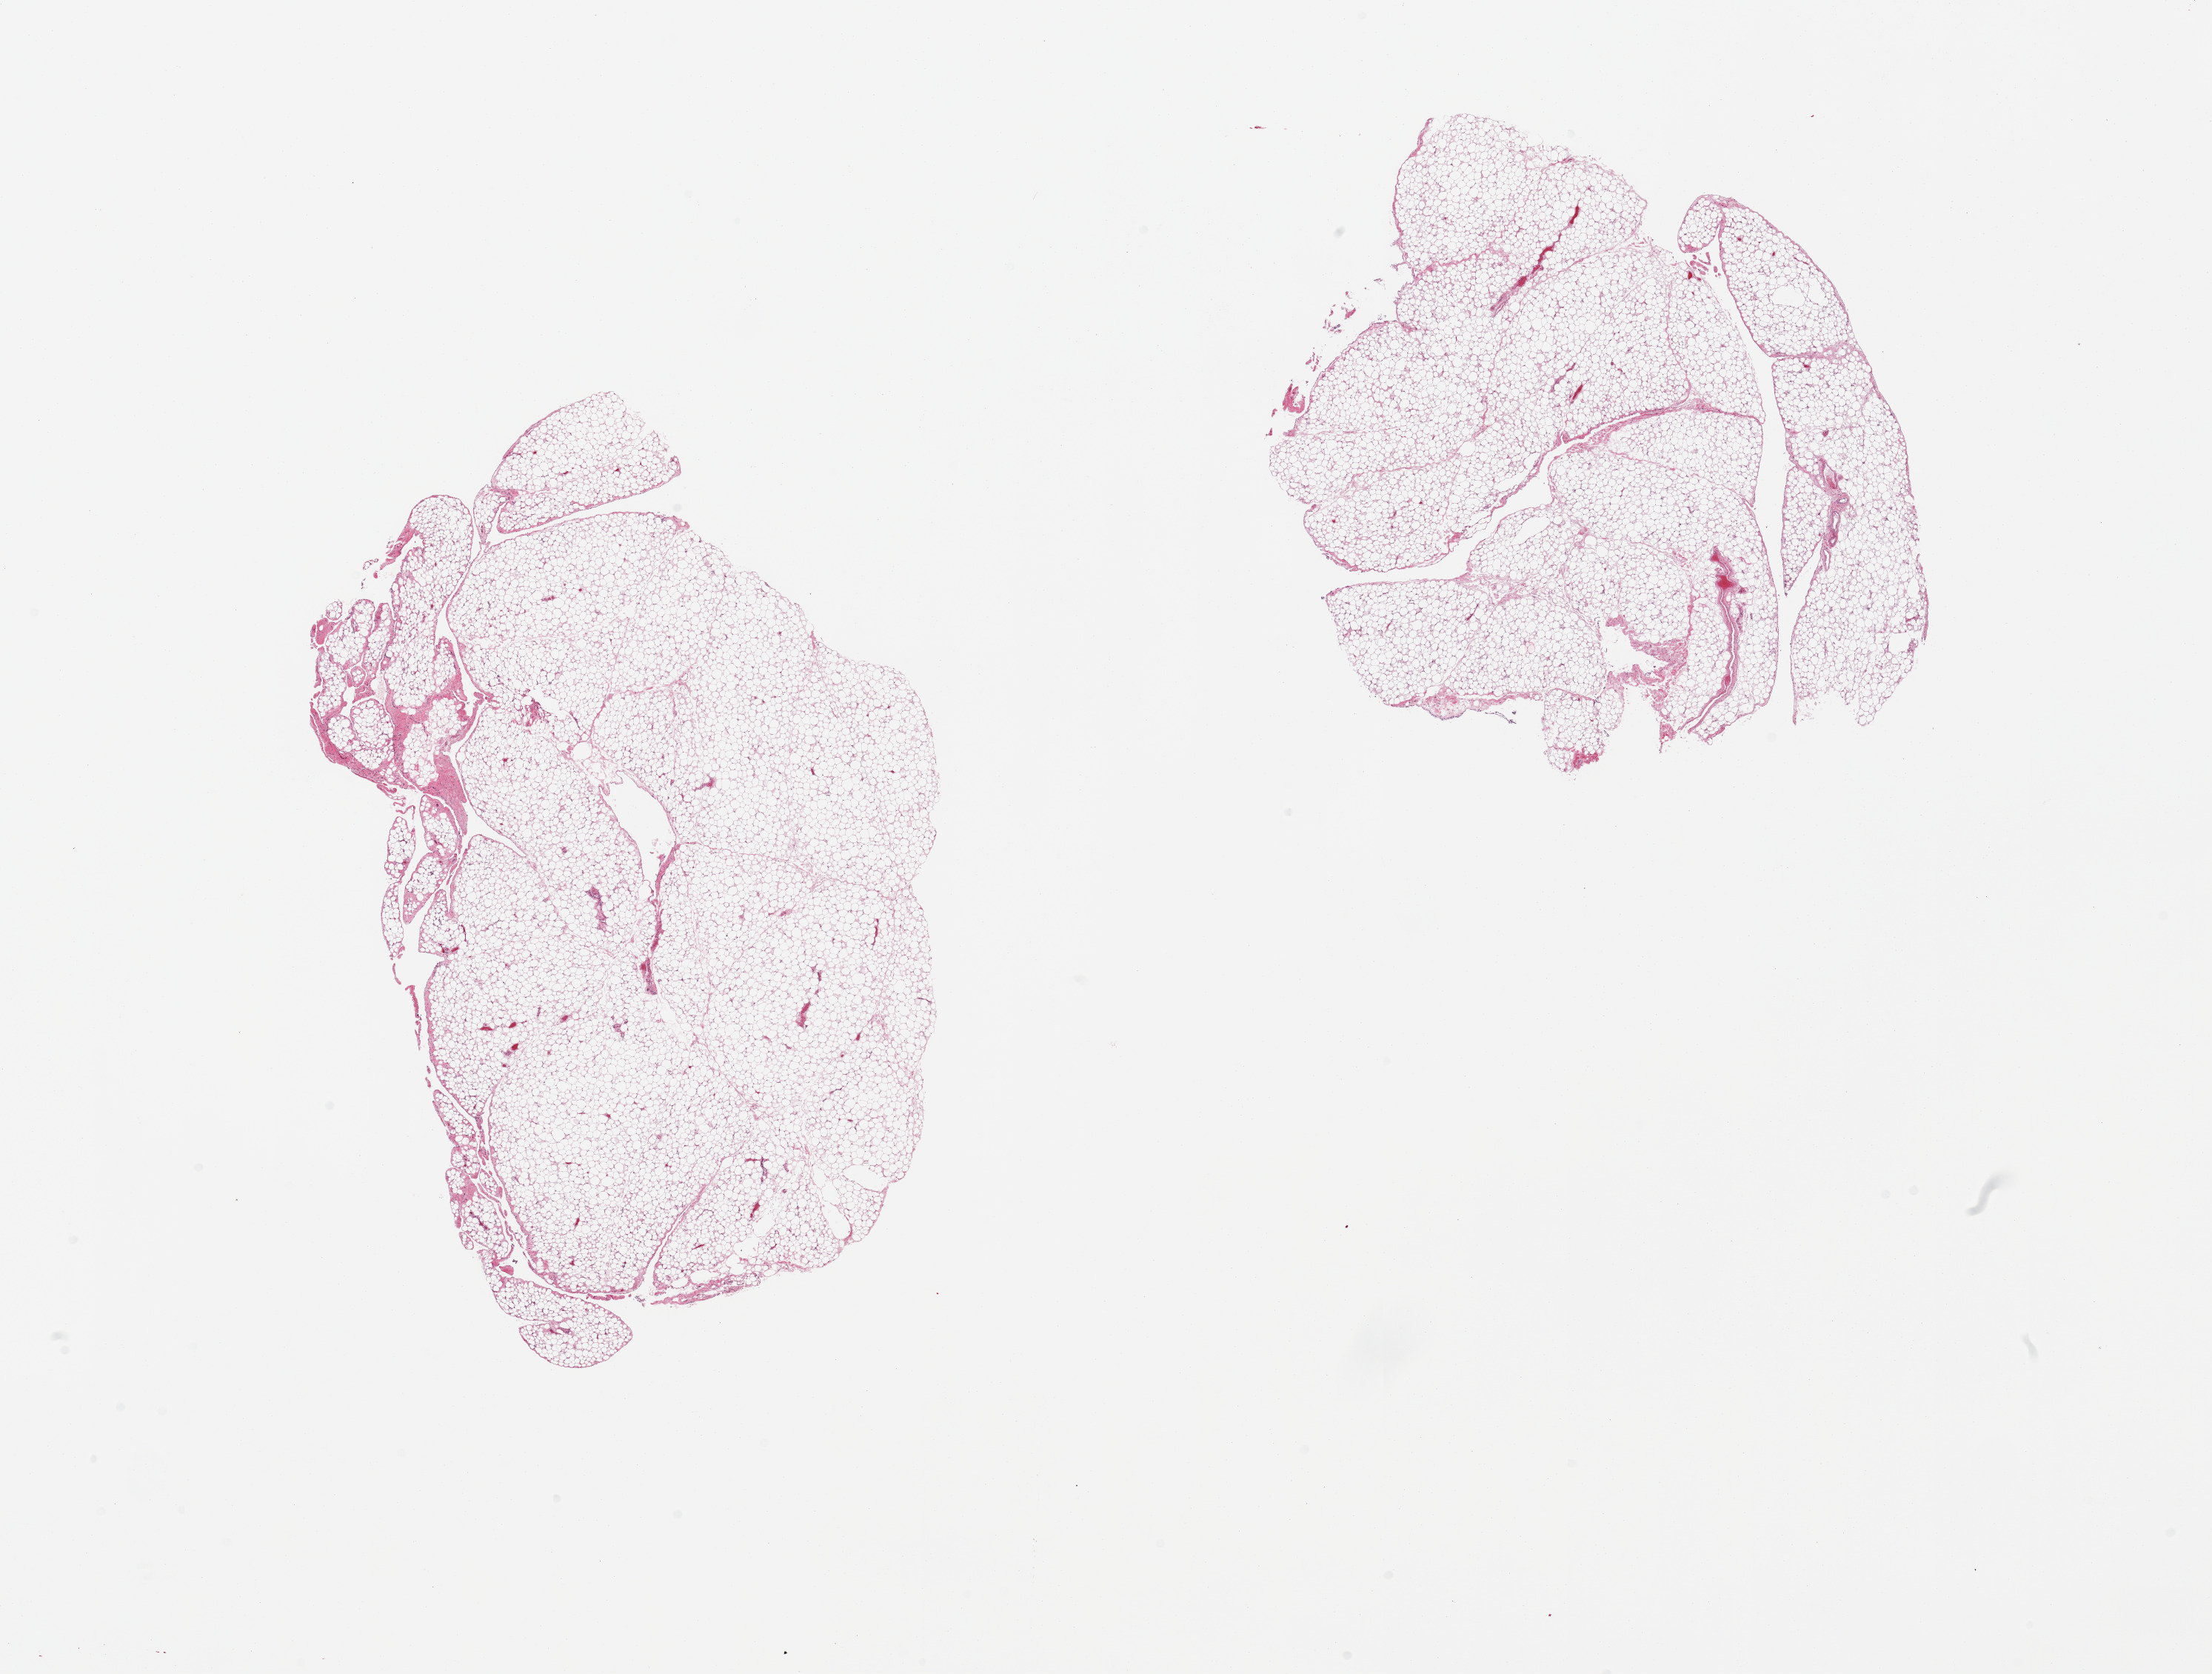
Digitized haematoxylin and eosin-stained section — low-resolution overview of the scanned area, about 23.6 x 17.9 mm. PAXgene-fixed paraffin-embedded (PFPE) section. Section of omentum (target tissue). Tissue donor sample. Donor: female.
Pathologist's review note for this sample: 2 pieces, minimal fascia/vascular tissue.